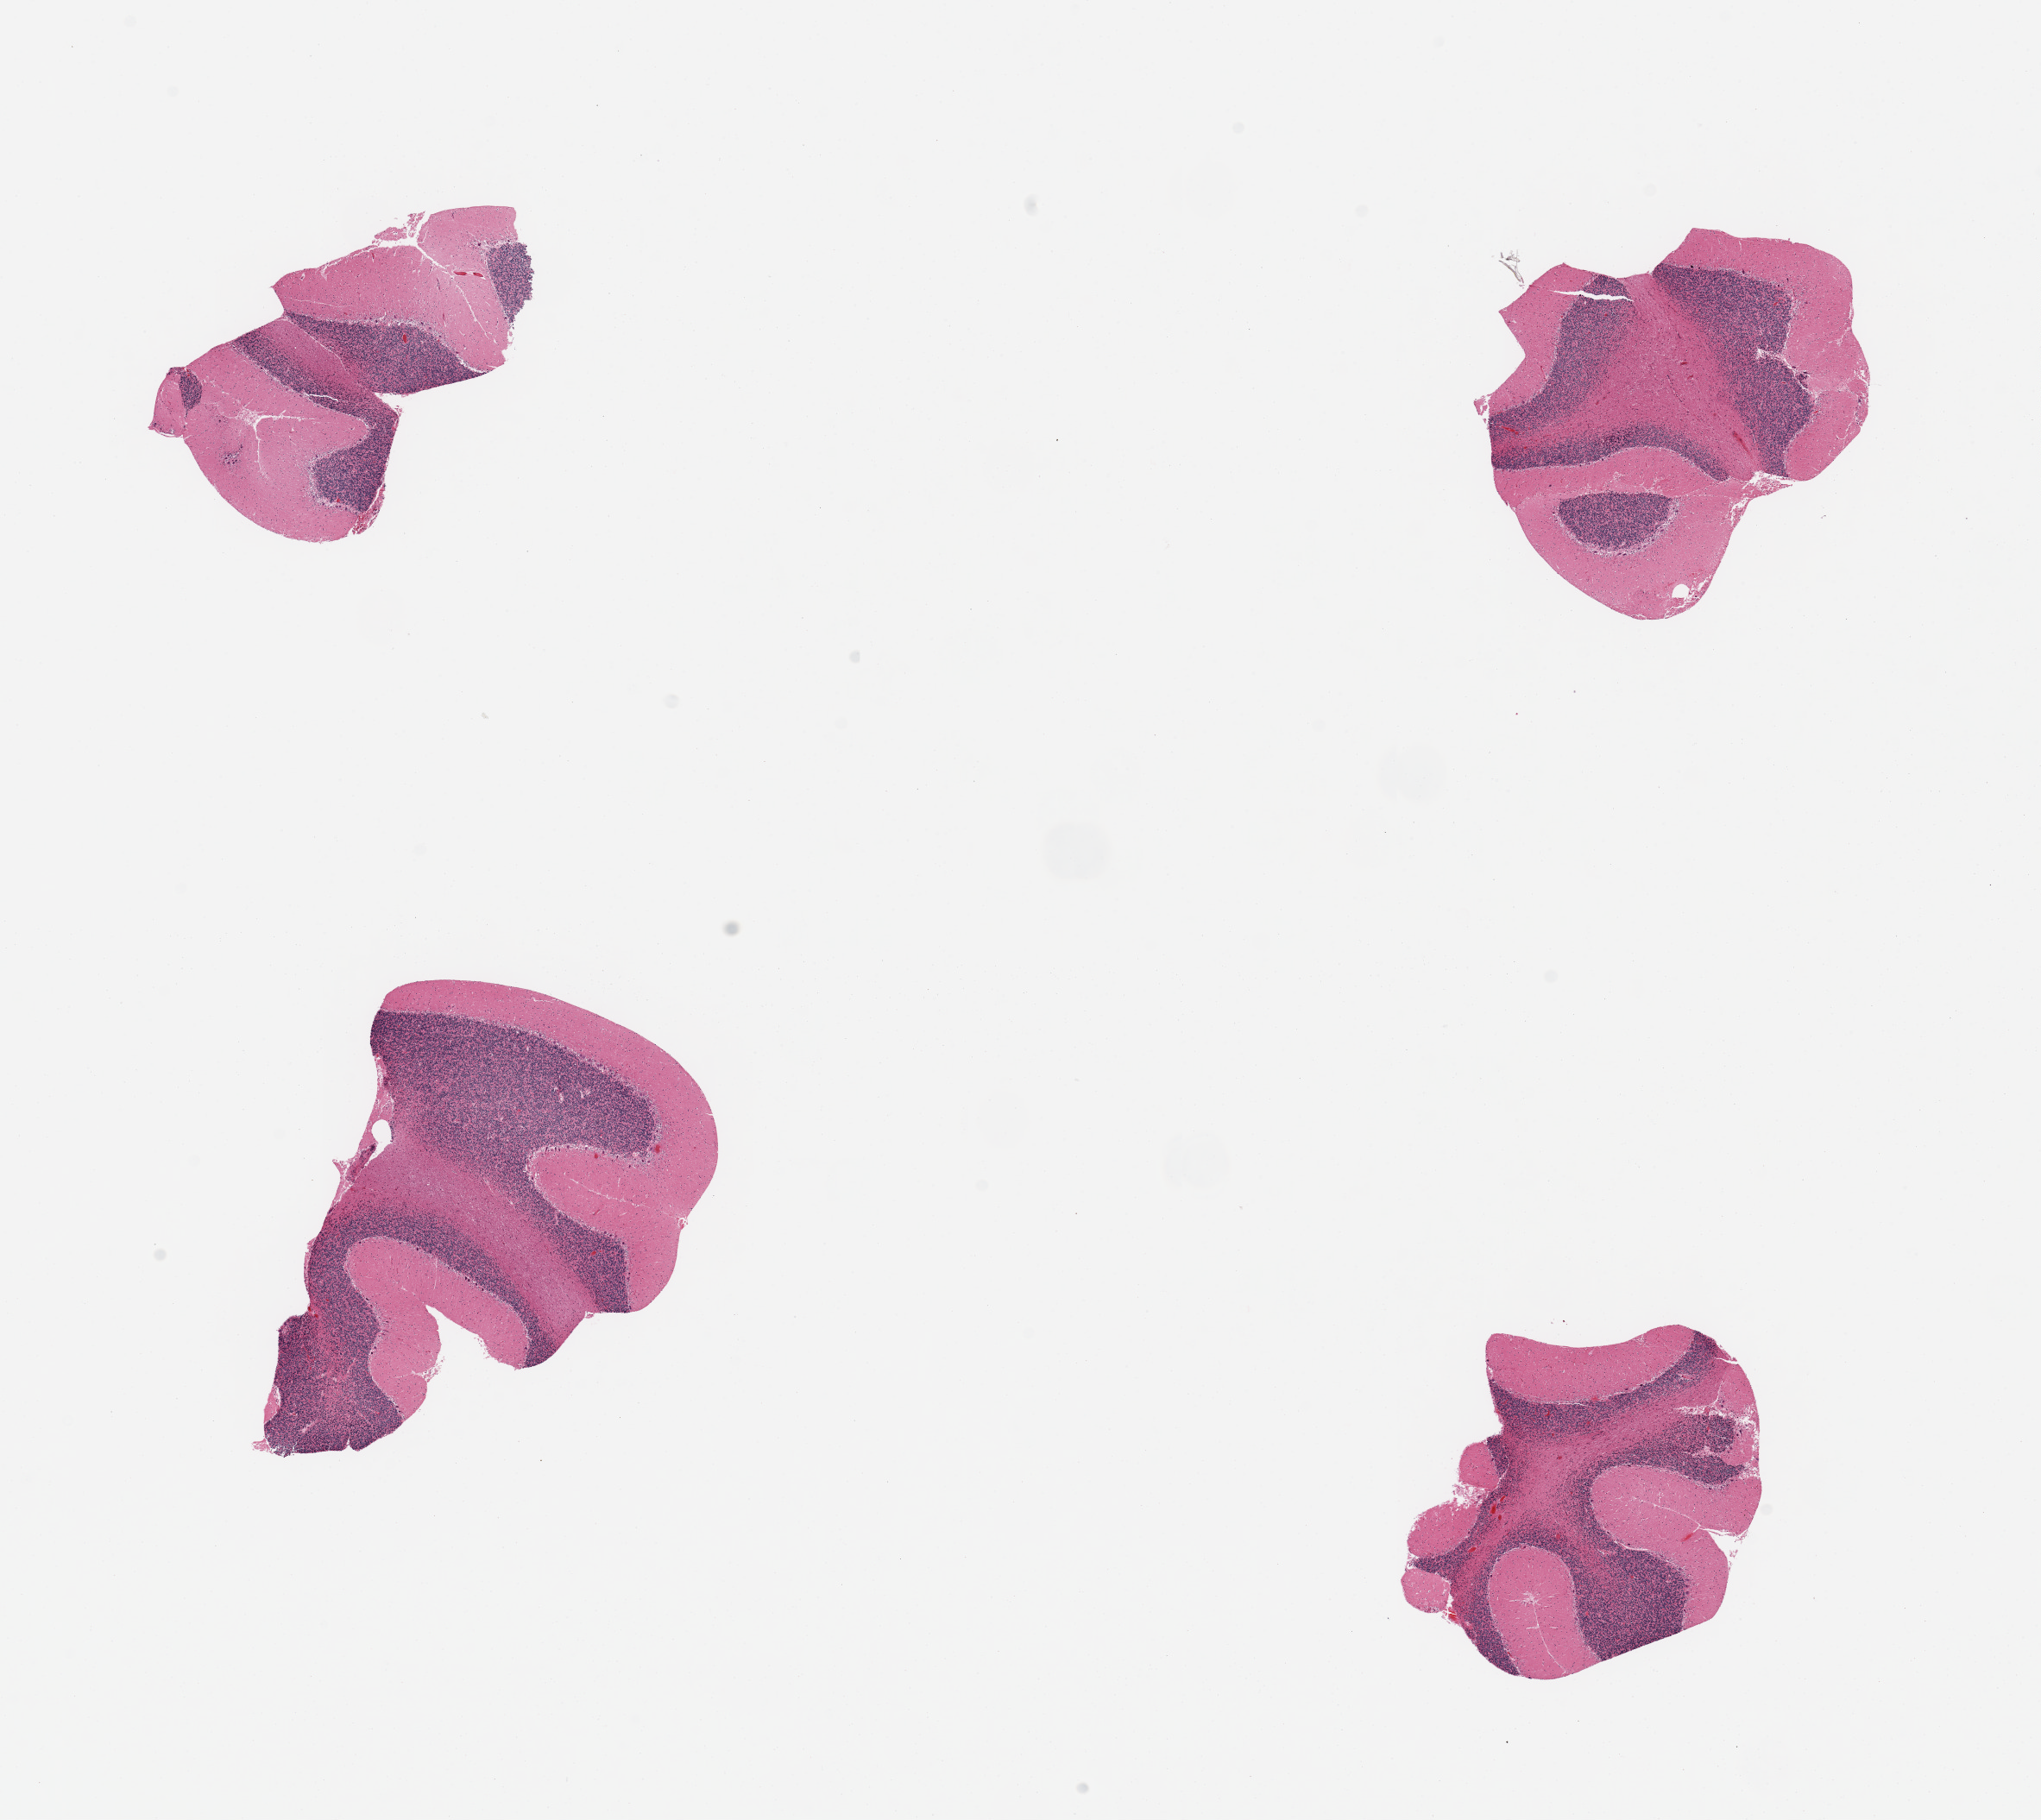
Digitized hematoxylin and eosin (H&E)-stained section — a low-resolution overview of the entire scanned area, about 18.7 x 16.7 mm; PAXgene-fixed, paraffin-embedded tissue; sampled site (target tissue): cerebellum; tissue donor sample.
• pathologist's review note for this sample: 4 pieces; Purkinje cells present